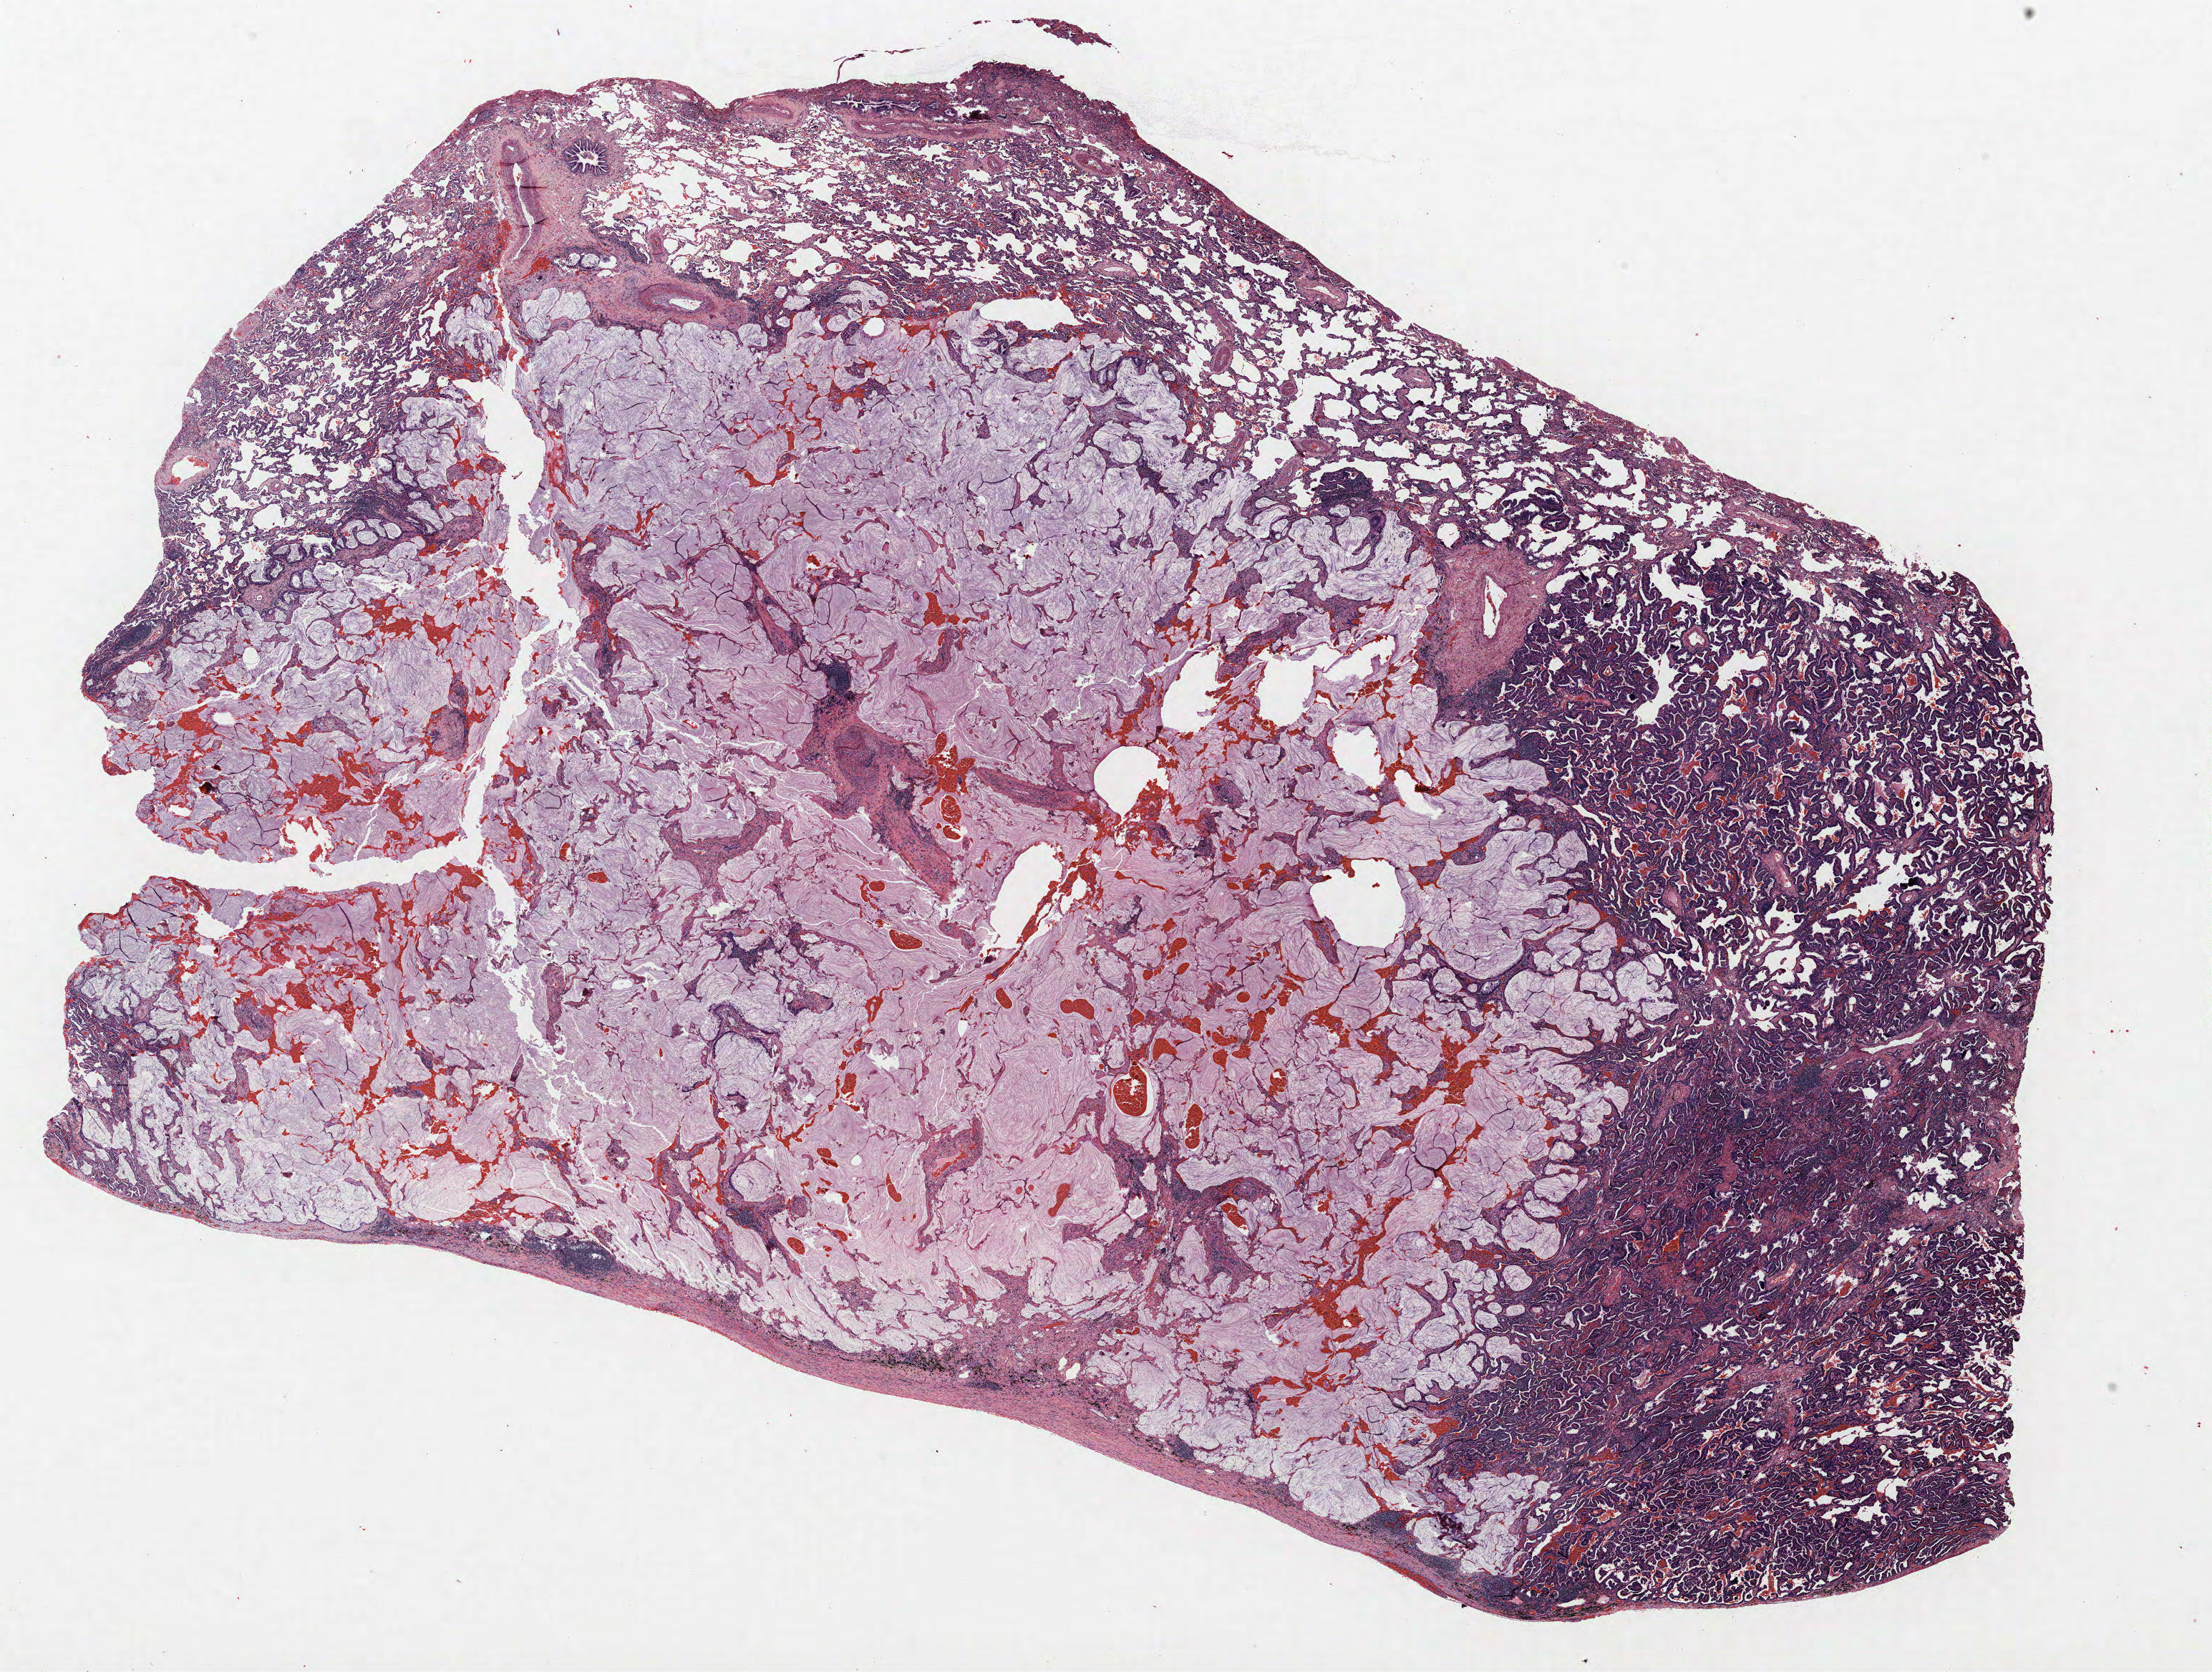
Whole-slide histology image, H&E-stained — a low-resolution overview of the entire scanned area, about 24.7 x 18.7 mm (slide scanned at 40x), formalin-fixed paraffin-embedded (FFPE) section, lung tissue. Male, age 67 at enrolment. Grade: well differentiated (G1).
Participant's lung-cancer diagnosis: Bronchiolo-alveolar carcinoma, non-mucinous (ICD-O-3 8252/3). ICD-O-3 topography: lower lobe of lung (C34.3). Stage (AJCC 6th edition): IB. Primary tumour location (clinical record): right lower lobe. Tumour size (pathology): 65 mm.